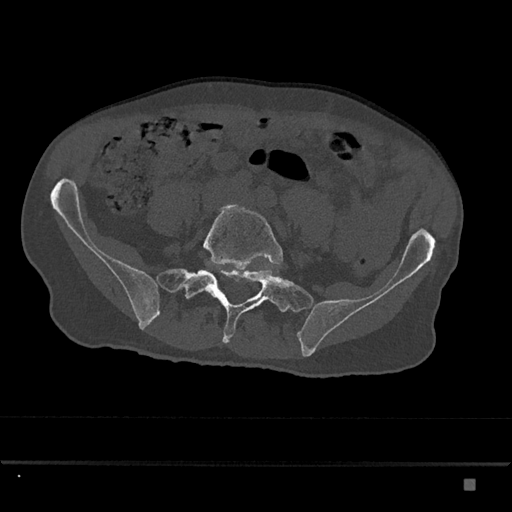
CT including the spine, one axial slice; position 251 of 797 along the scan axis; reconstruction kernel Br40s/3; bone window (W 1800 / L 400 HU); 0.5 mm slice thickness; 512 × 512 image matrix. Patient: male, 72 years. From the clinical record (not read from this slice): primary cancer: prostate.
Outlined on this slice (semi-automatic segmentation, software-assisted and operator-edited):
- L5 vertebra: box from (x=203, y=204) to (x=283, y=293) px